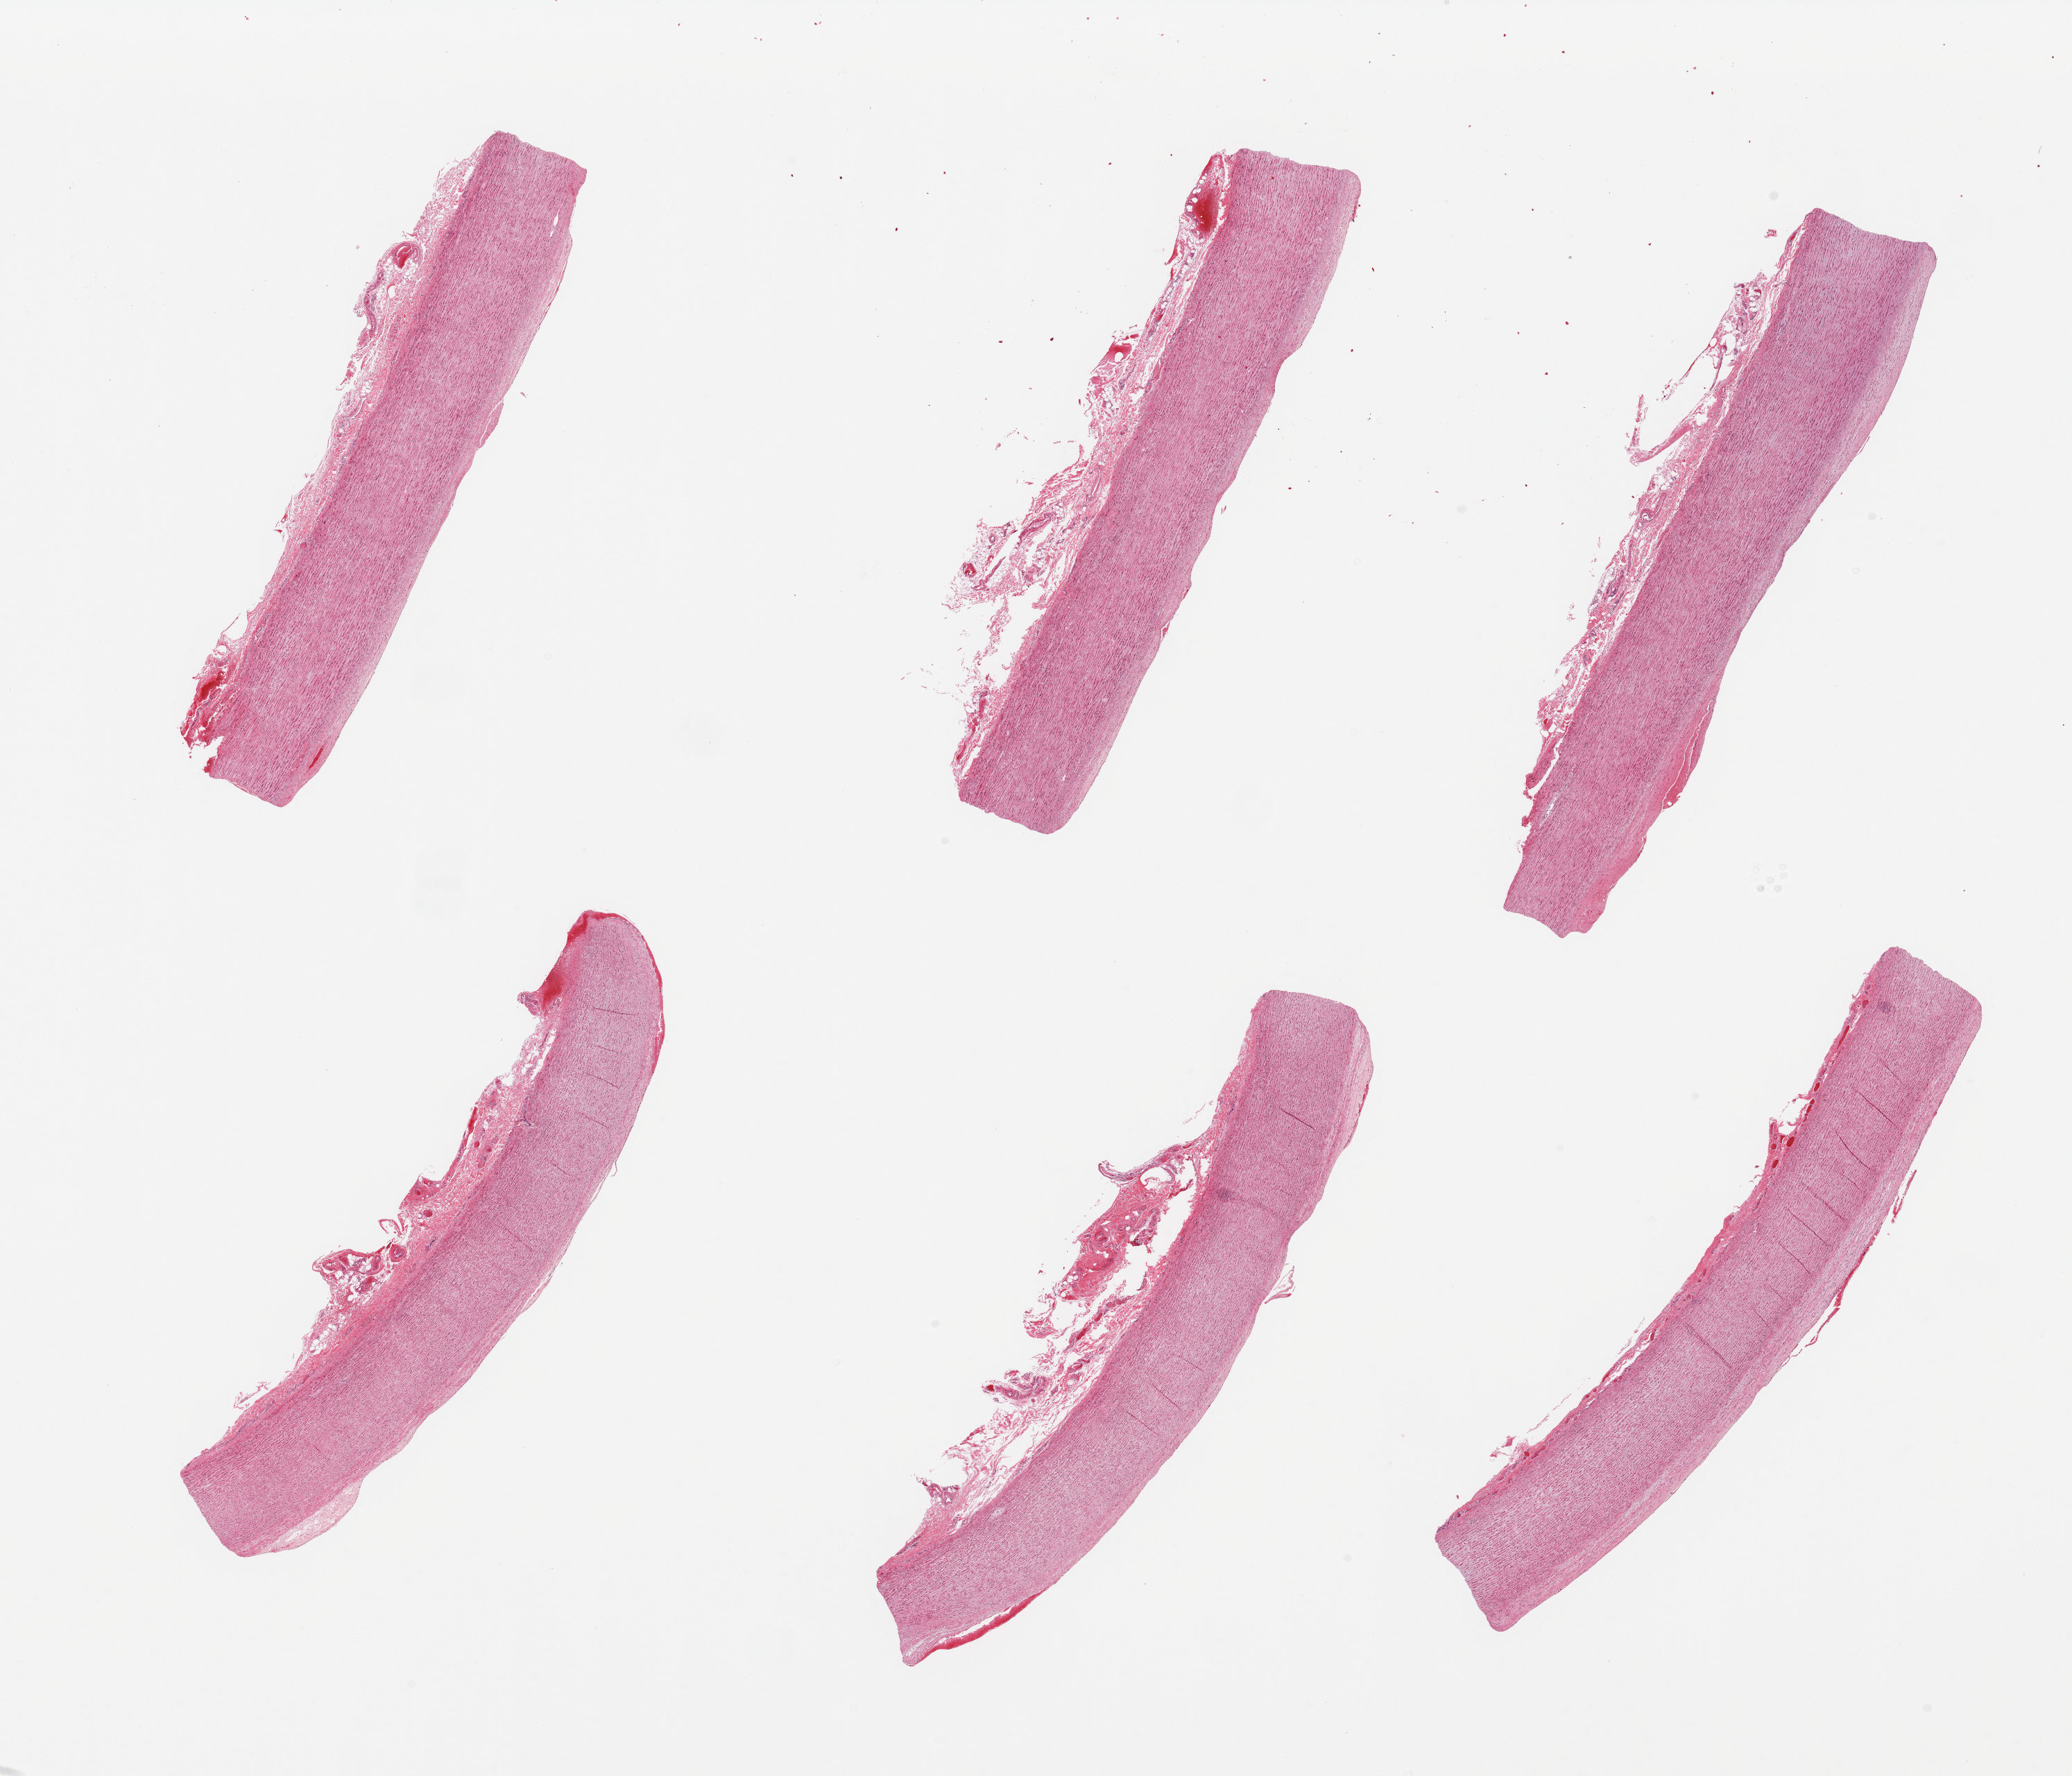
Whole-slide image, haematoxylin and eosin stain, brightfield — a low-resolution overview of the entire scanned area, about 23.6 x 20.2 mm (acquisition: 20x scan). PAXgene-fixed paraffin-embedded (PFPE) section. Target tissue: aorta. Donor tissue sample. Donor sex: female.
- pathologist's review note for this sample: 6 pieces, focal atherosis up to ~0.3mm